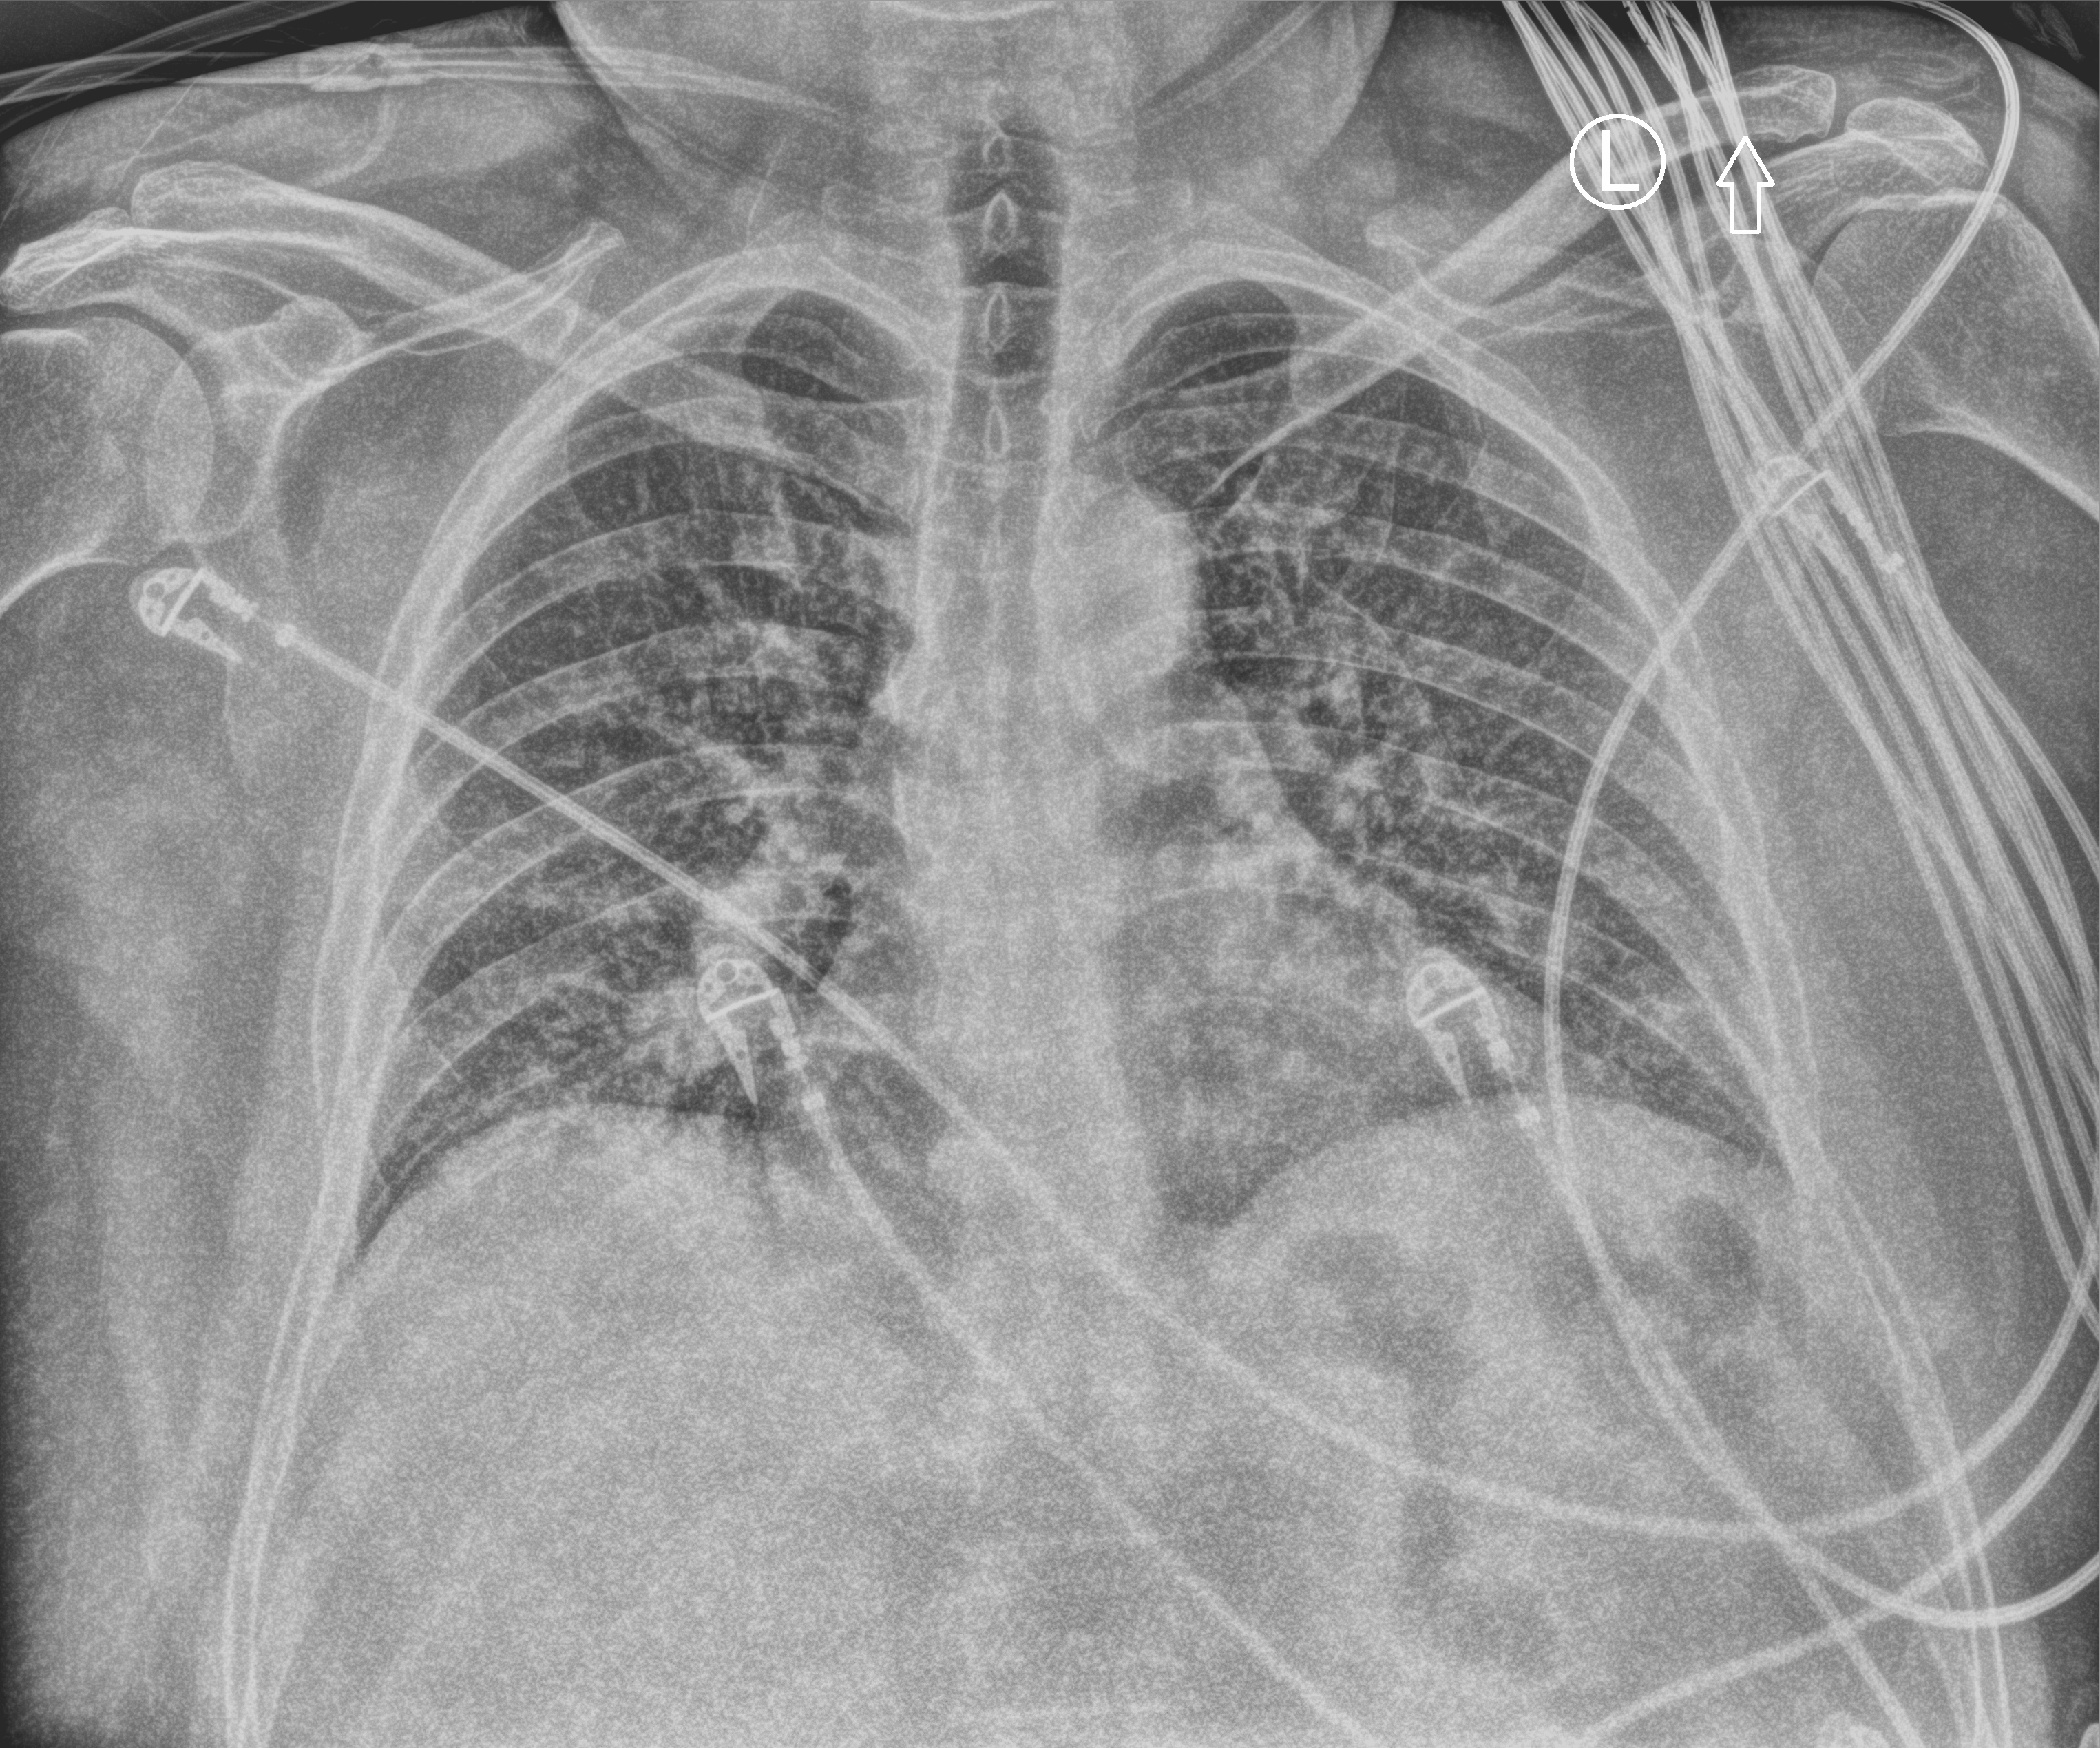
Bedside chest radiograph (computed radiography). Male patient hospitalised with COVID-19, age 18–59 years.
Hospital-stay facts (about this admission, not read from this image; timing relative to this image not recorded):
- other chronic lung disease (admission record): yes